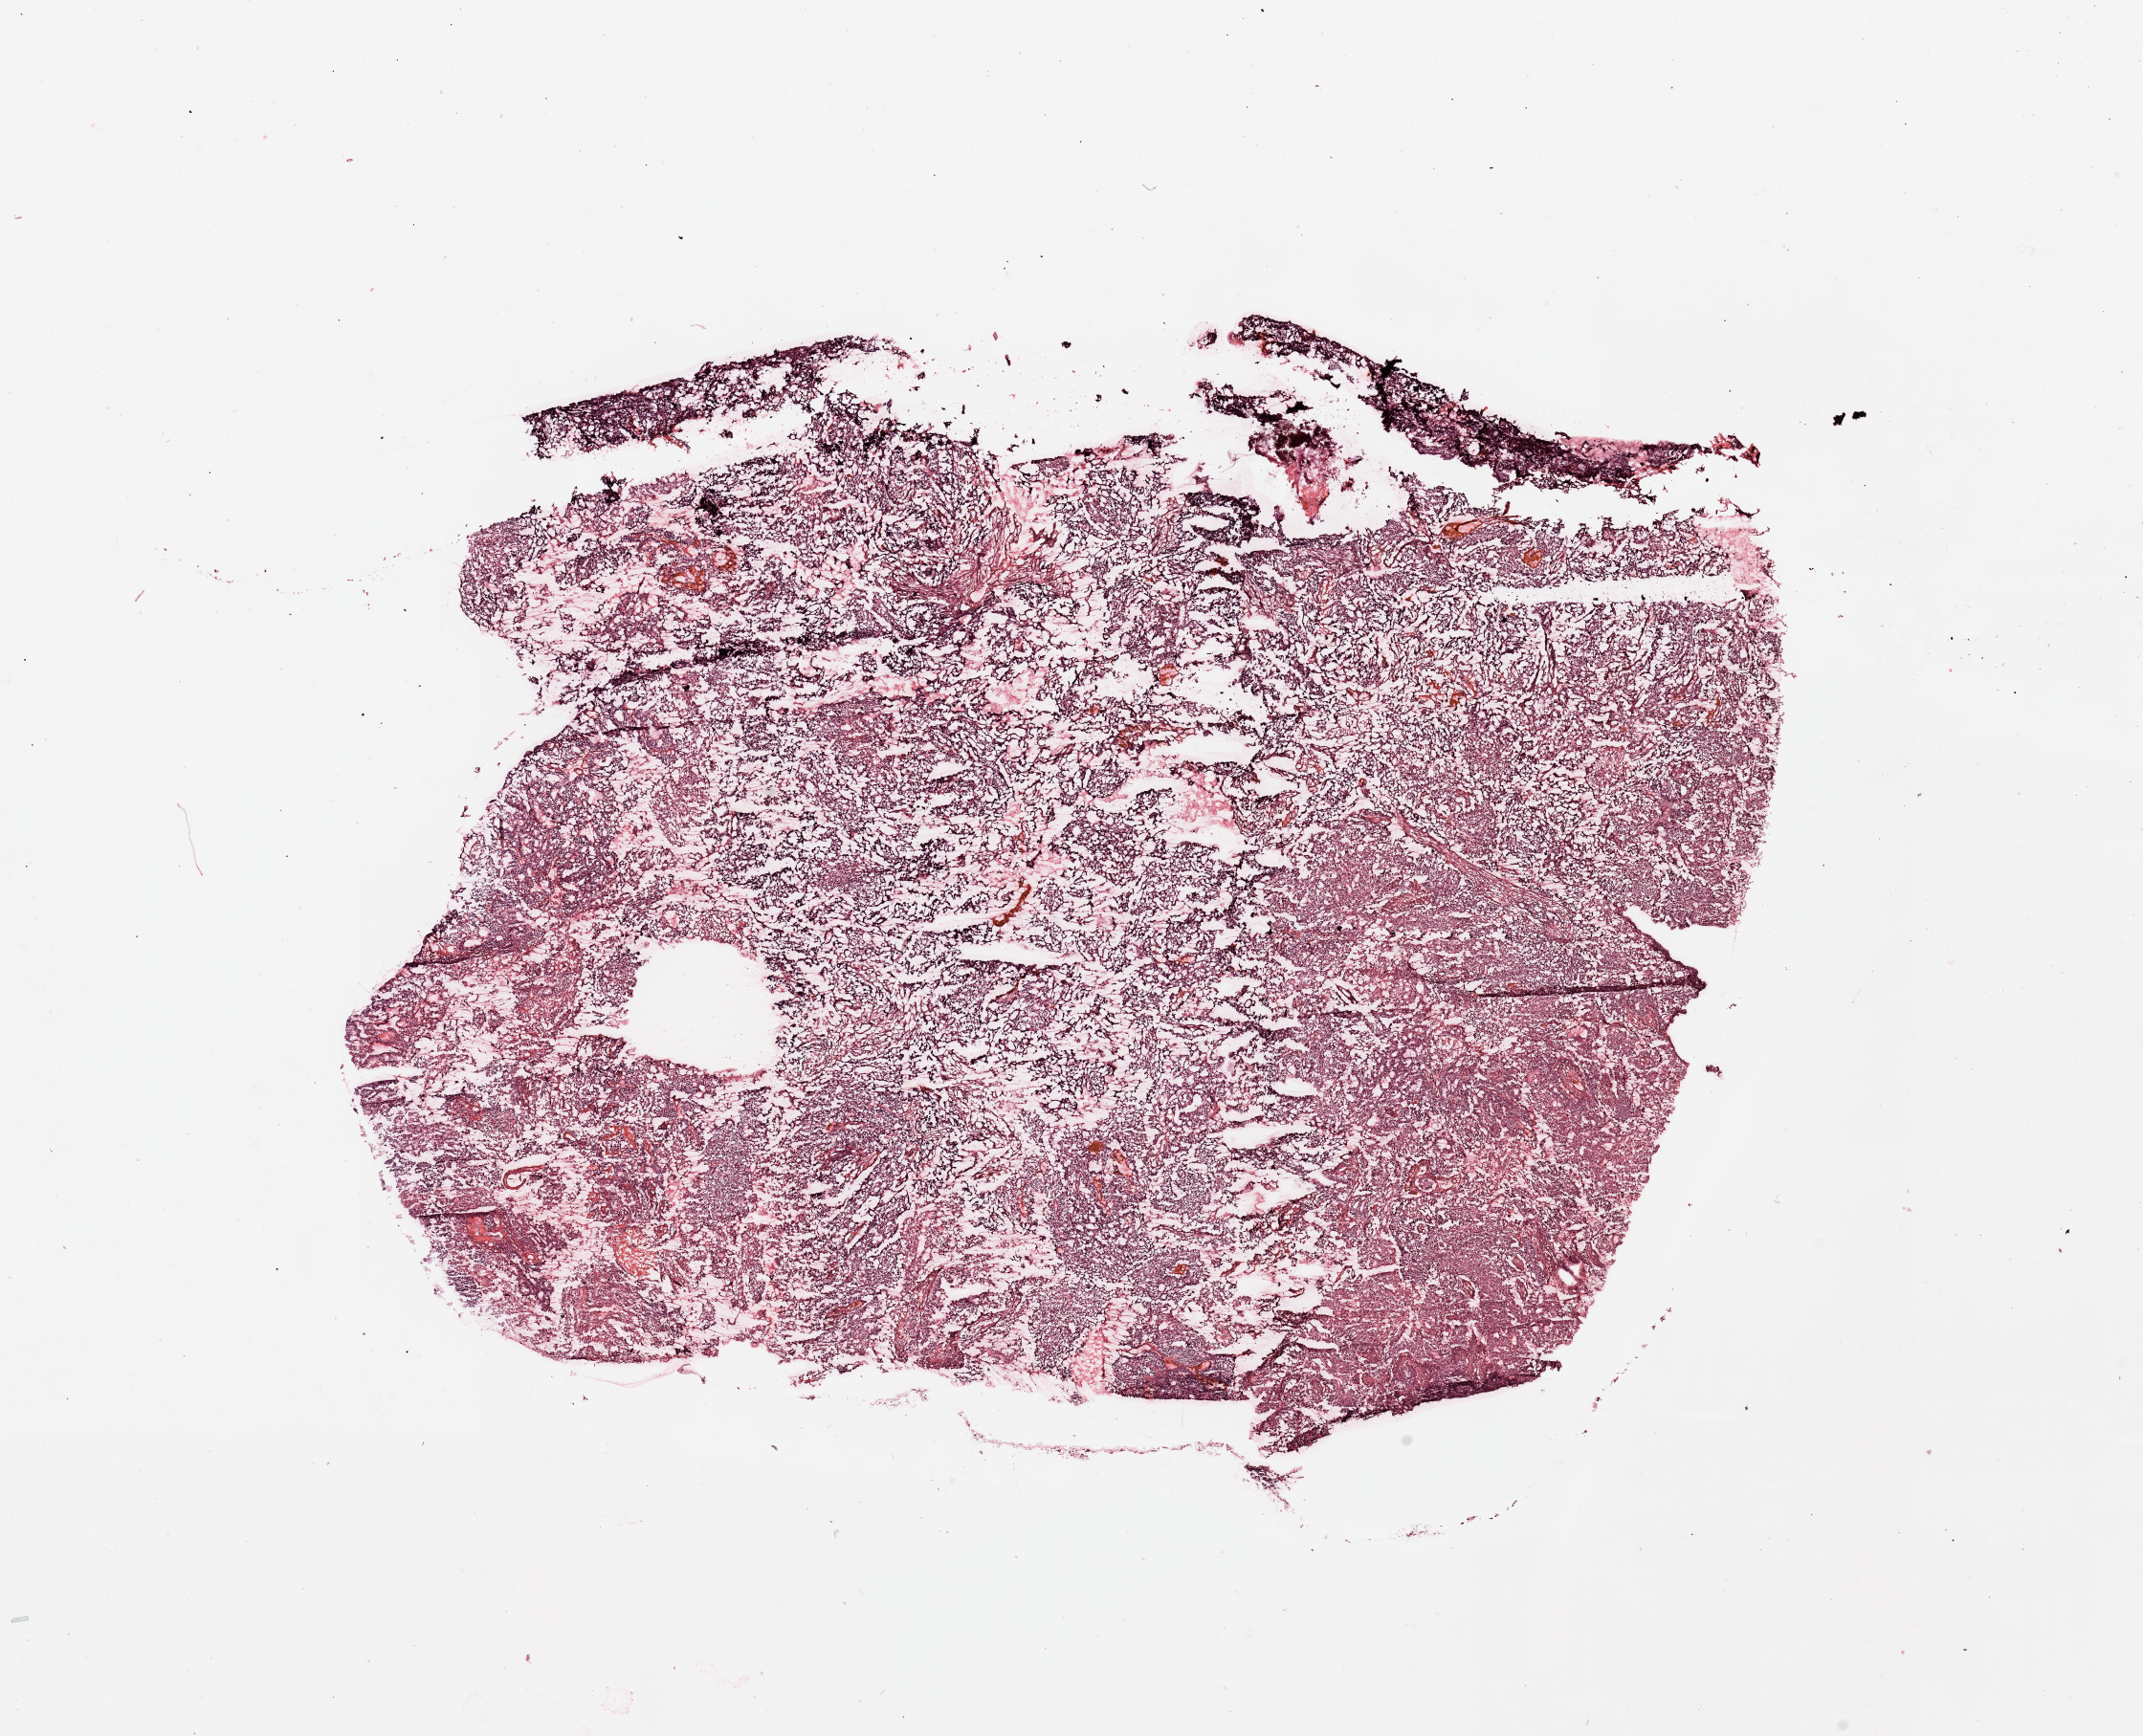
Whole-slide histology image, H&E-stained — whole scanned area (about 17.7 x 14.4 mm, acquisition: 20x scan) shown as a low-resolution overview. Tumour tissue sample, sampled site: uterus. Female, 67 y/o. Pathologist review of this section (percent, as recorded): tumour nuclei 95%, necrosis 0%.
Histologic diagnosis: Endometrioid adenocarcinoma, NOS.